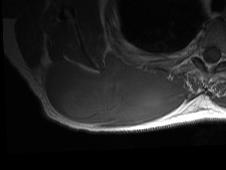
MRI of an extremity soft-tissue mass, one axial slice. Position 30 of 81 along the scan axis. MR volume resampled by the dataset authors to the PET/CT grid (not the native acquisition matrix). 226 × 170 image matrix, field of view 221 × 166 mm. Male patient. From the clinical record (not read from this slice): histological type: pleiomorphic spindle cell undifferentiated; grade: high; site of the primary tumour: right parascapusular.
Structures marked on this image (expert contour drawn on MRI and transferred to this co-registered scan by the dataset authors):
- gross tumour volume including surrounding oedema: bounding box <44,54,187,128> (left, top, right, bottom; pixels)
- gross tumour volume (mass): <44,54,170,125>